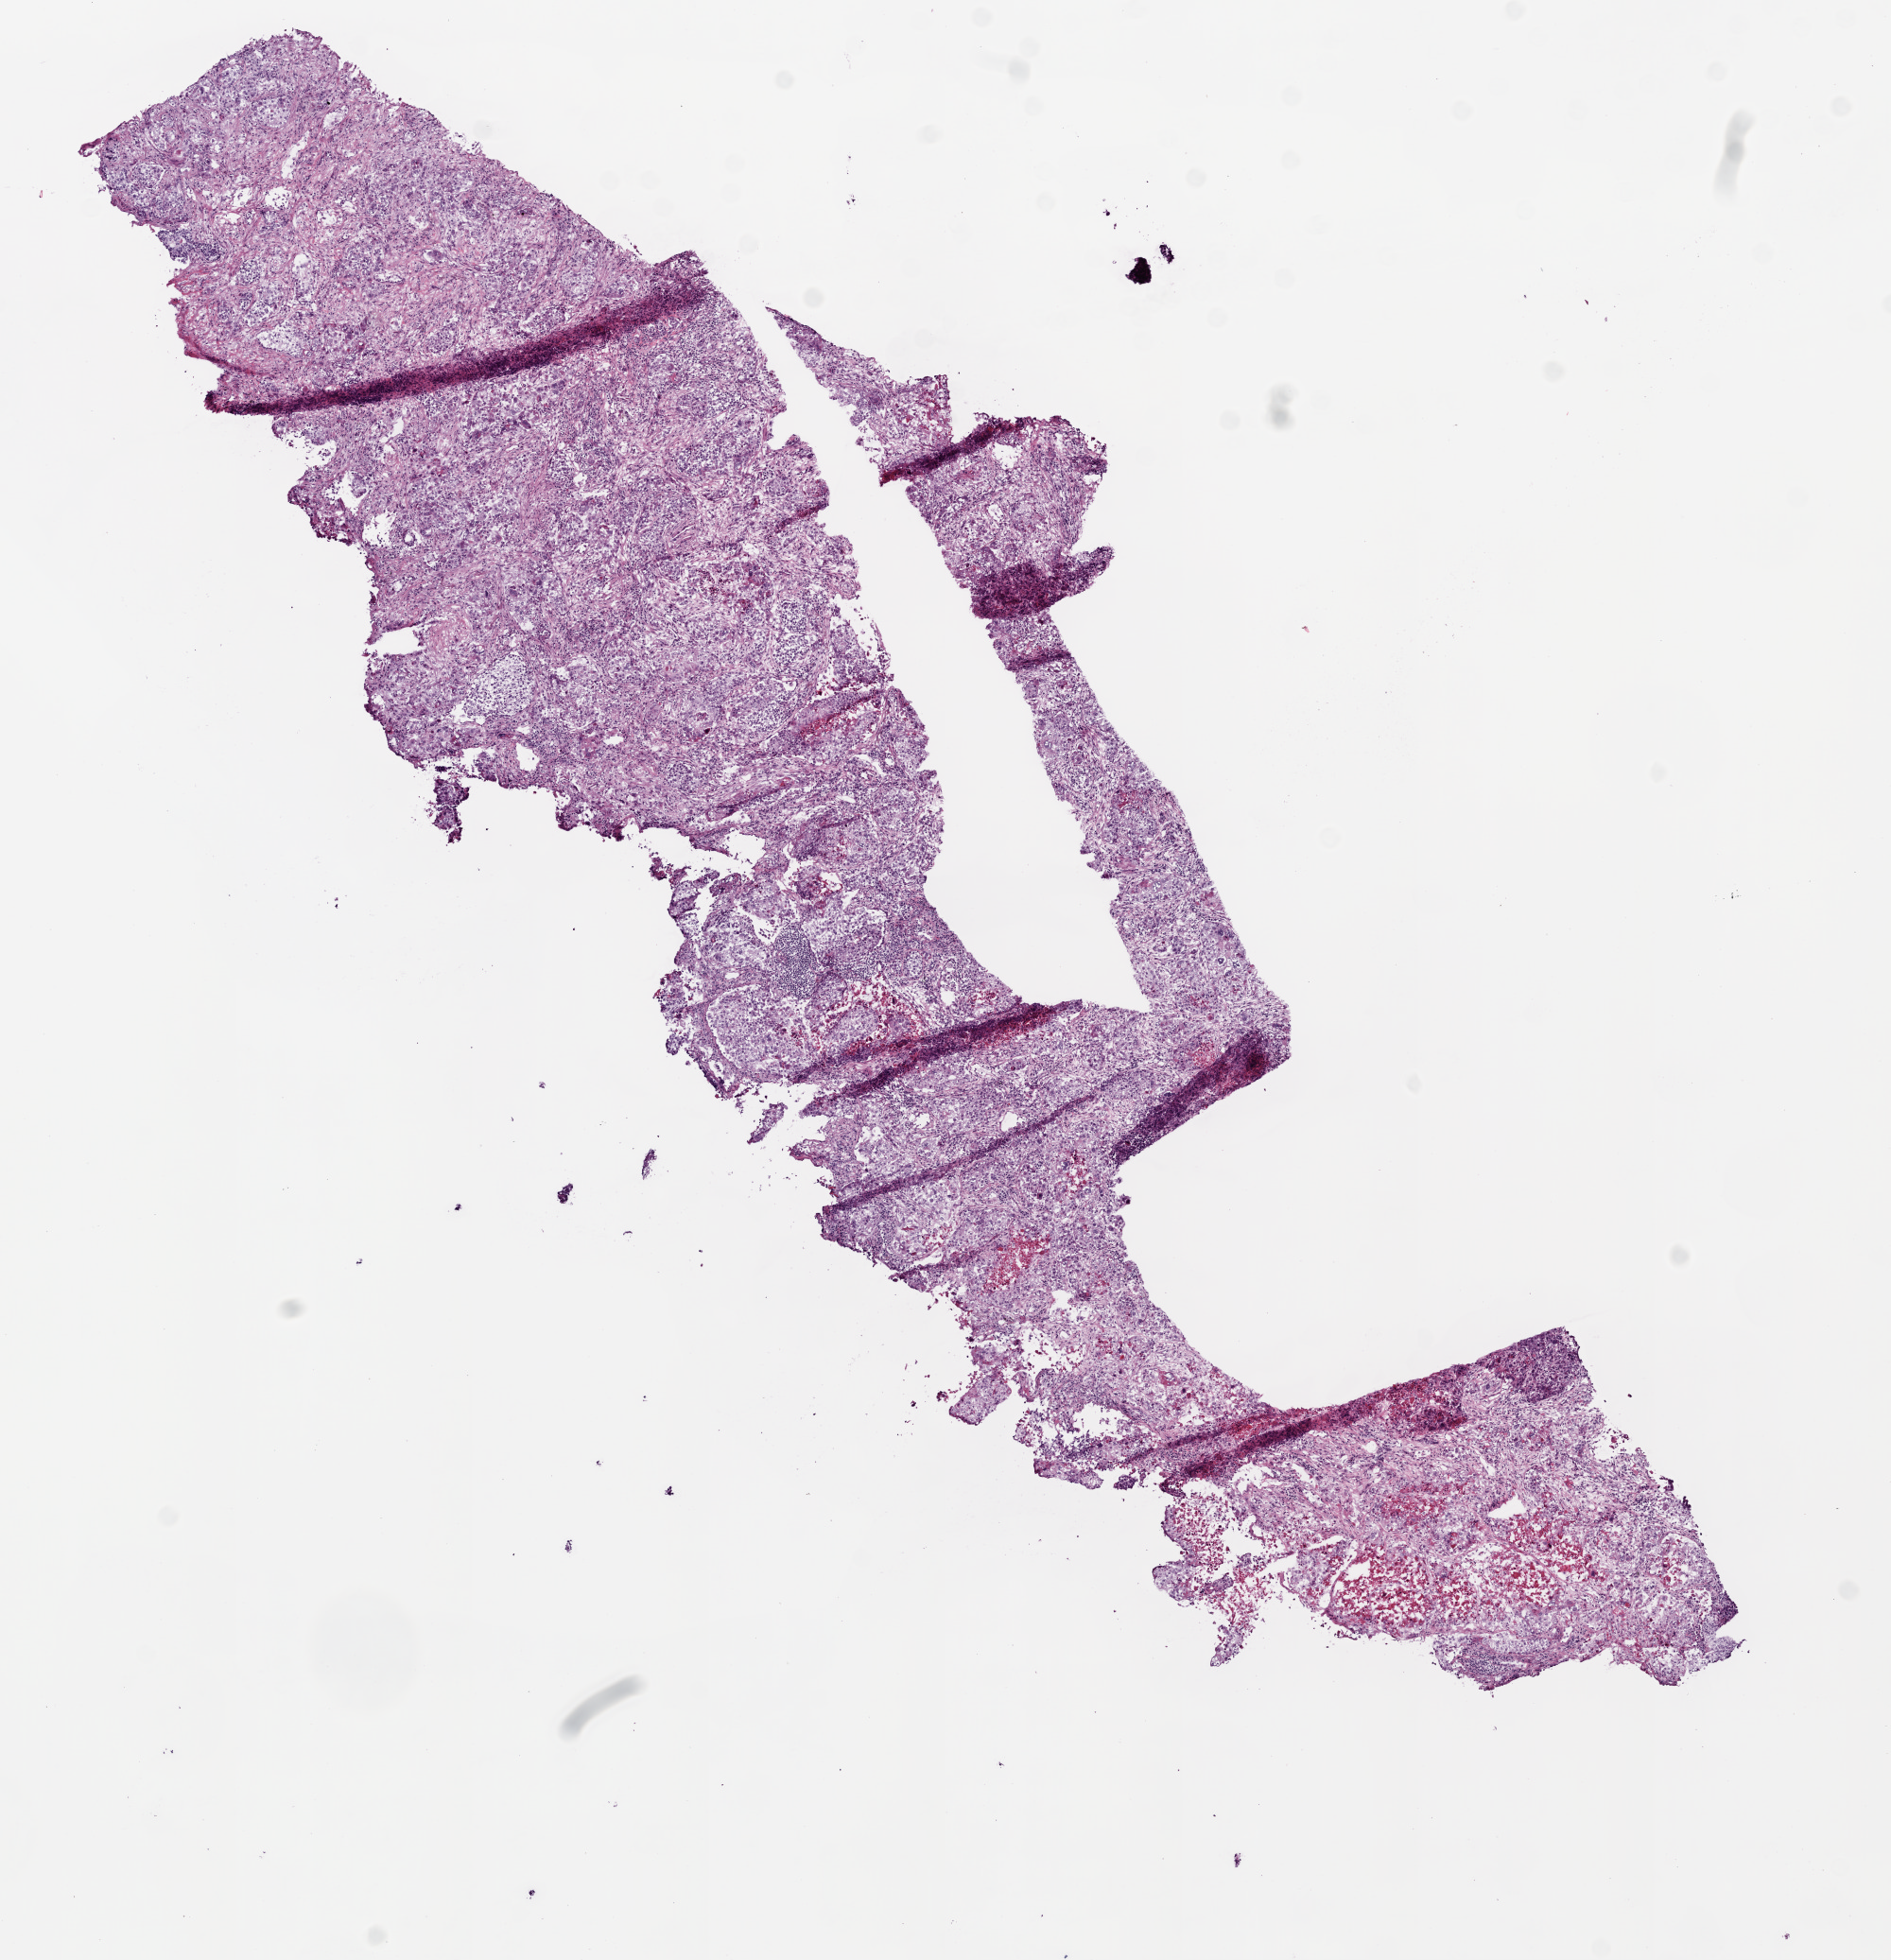
H&E whole-slide image — whole scanned area (about 8.0 x 8.3 mm, from a 20x scan) shown as a low-resolution overview; frozen section from the bottom of the tissue portion; lung, primary tumour sample. Male patient; age at initial diagnosis 57 years.
Pathologic diagnosis: Squamous cell carcinoma, NOS (lower lobe, lung).